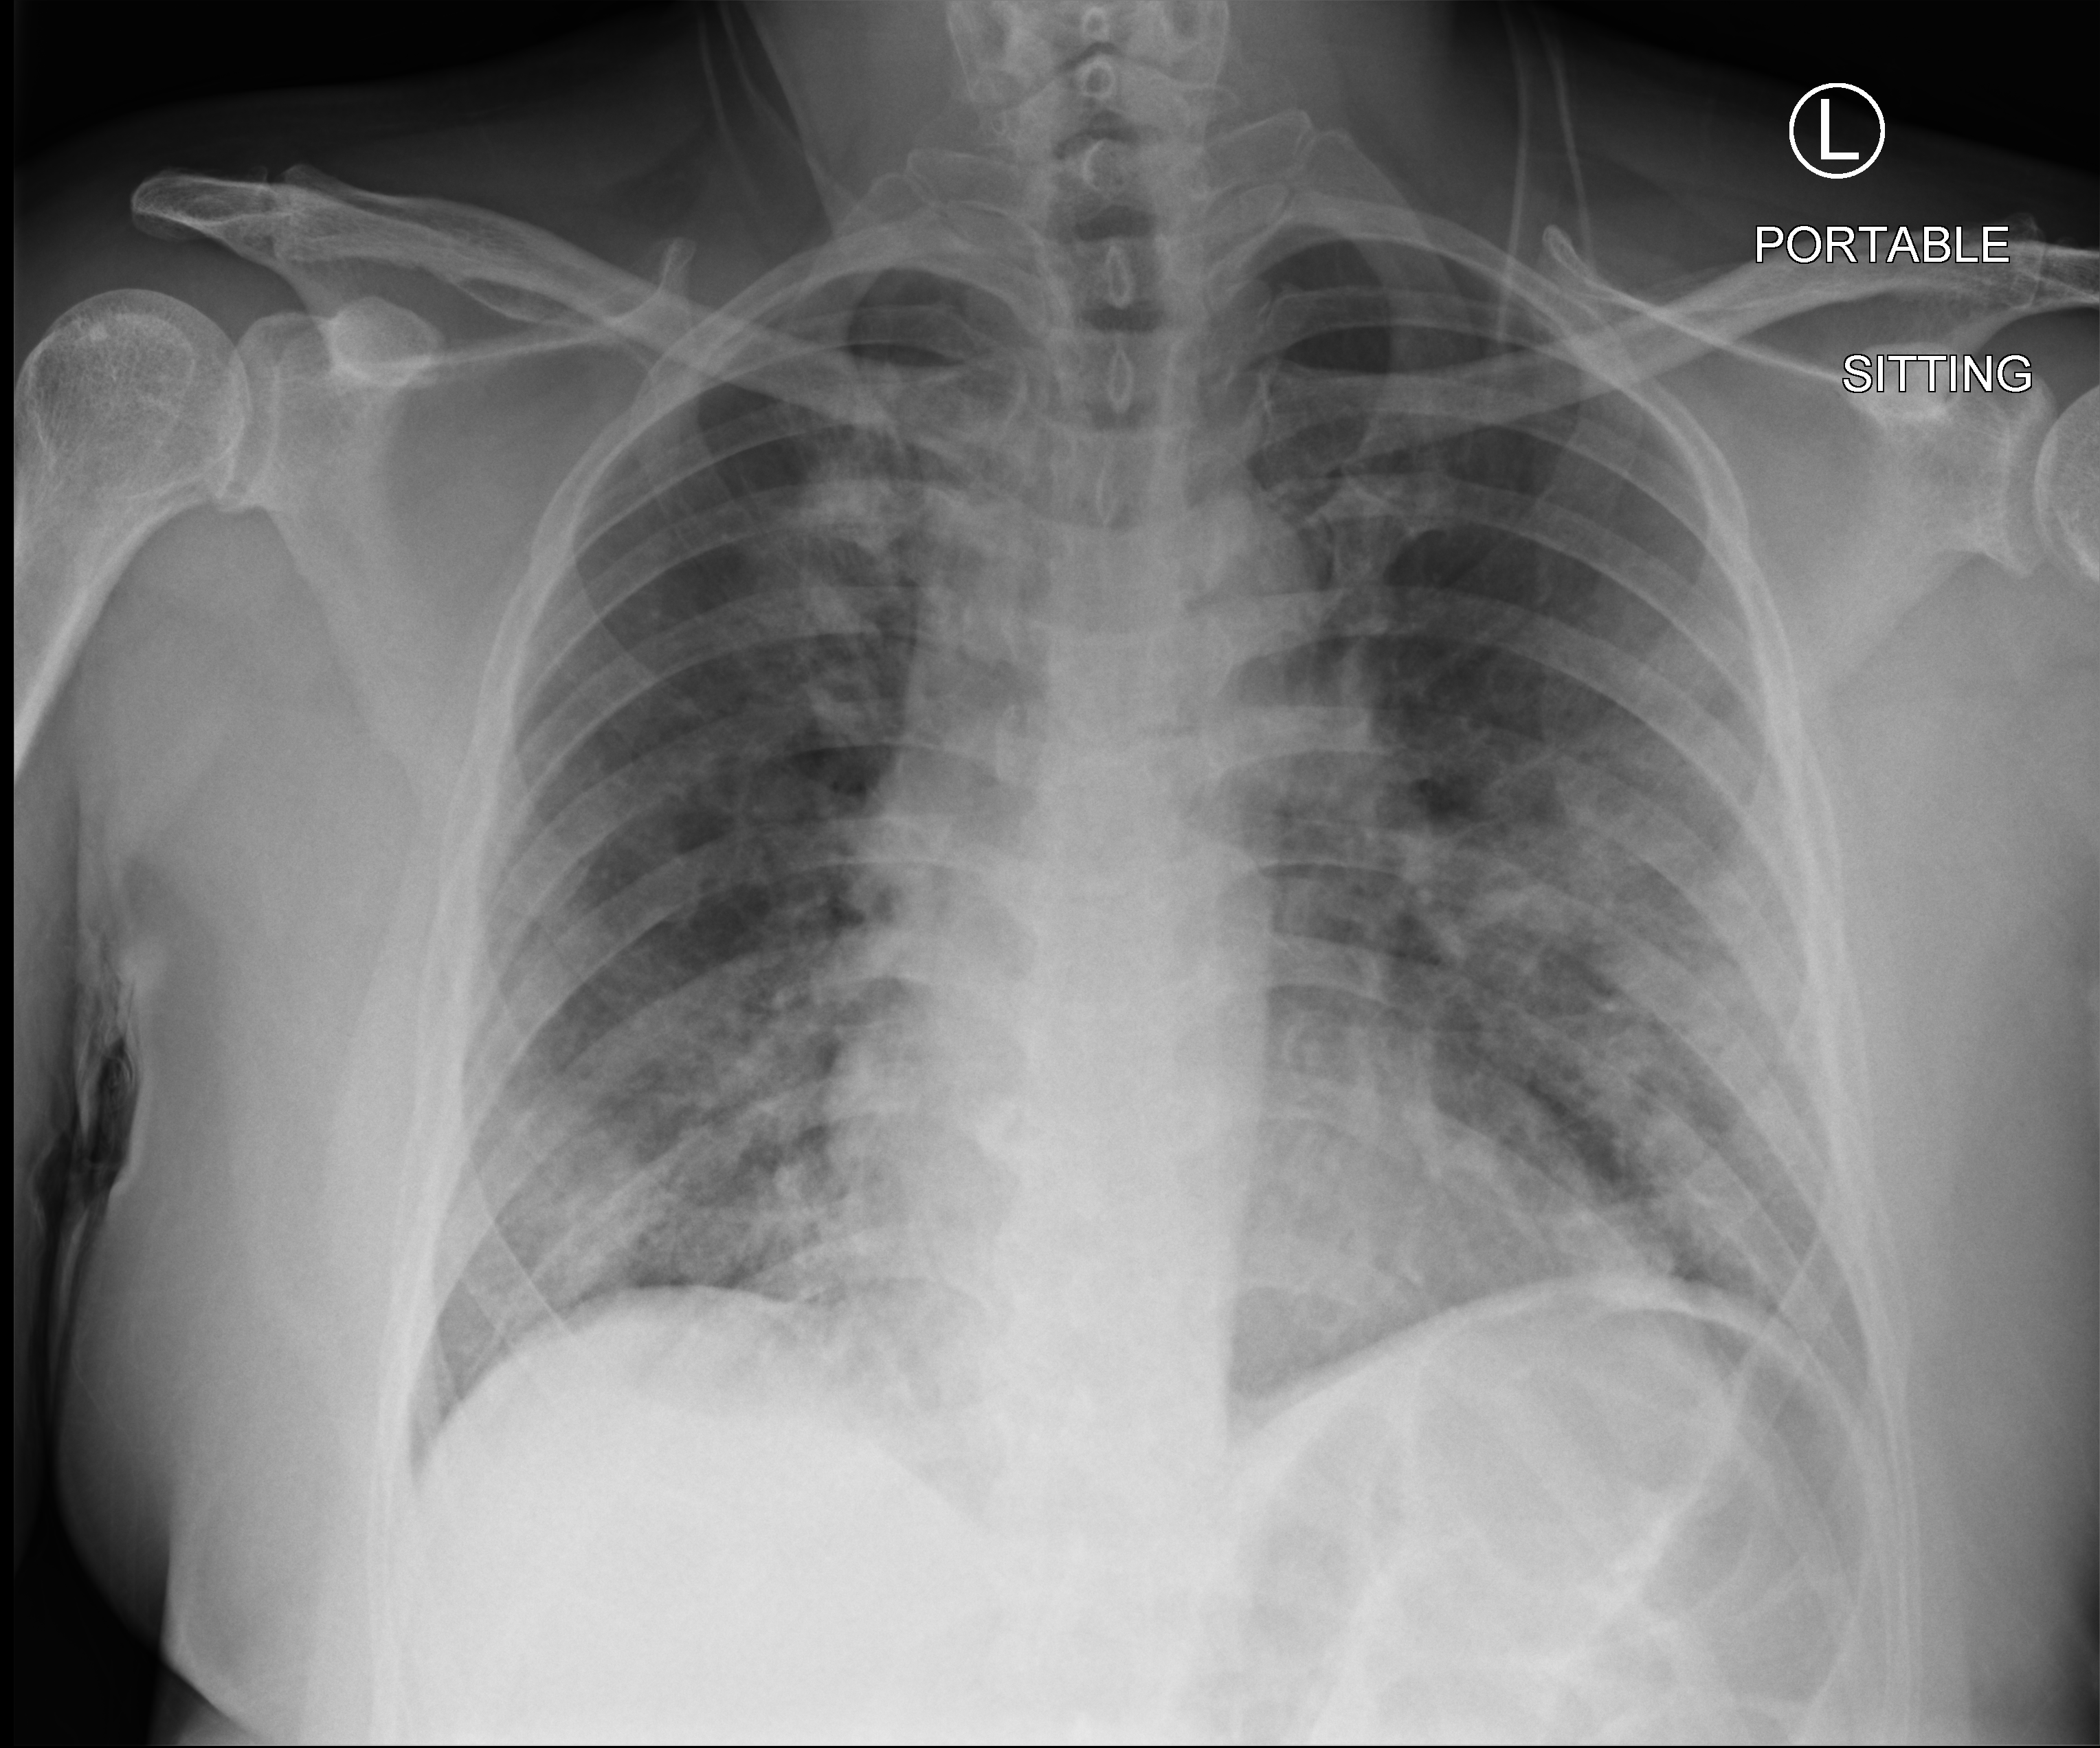
Chest X-ray (portable). Patient hospitalised with COVID-19; male, aged 18–59 years.
Hospital-stay facts (about this admission, not read from this image; timing relative to this image not recorded): mechanically ventilated during this hospital stay: no; admitted to intensive care during this hospital stay: no.